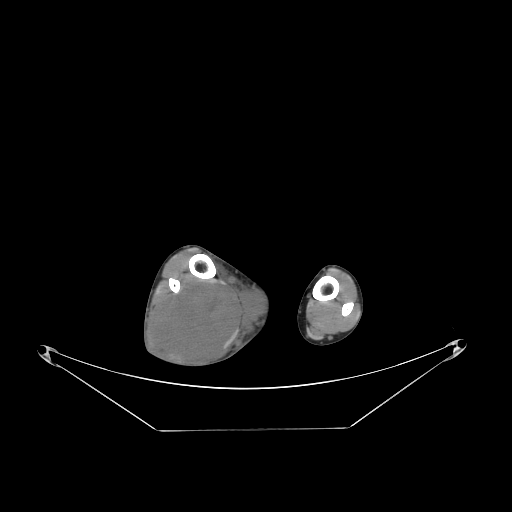
CT of an extremity soft-tissue mass (from a PET/CT study), one axial slice; position 69 of 267 along the scan axis; reconstruction kernel STANDARD; 140 kVp; soft-tissue window (W 400 / L 40 HU); 512 × 512 image matrix. Male patient. Case-level facts recorded for this patient, not image findings: histological type: liposarcoma - round cell; grade: high; site of the primary tumour: right calf.
Structures marked on this image (expert contour drawn on MRI and transferred to this co-registered scan by the dataset authors):
- gross tumour volume (mass): bounding box <151,276,270,369> (left, top, right, bottom; pixels)